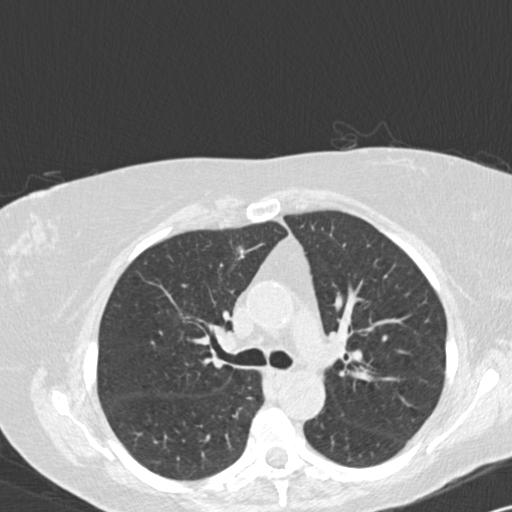
Low-dose screening chest CT, axial slice. Third annual screen. Lung window (W 1500 / L -600 HU). Standard (soft-tissue) reconstruction kernel (B30f). Slice 47 of 141 in the series. Female, age 72 years at enrolment.
- Lesion marked by an expert reader, bounding box (x1, y1, x2, y2) in pixels: (214, 232, 261, 281).
- Reader record for this screening exam (exam-level; its link to the box is not recorded): non-calcified nodule or mass ≥4 mm, right upper lobe, 8 × 8 mm, spiculated (stellate) margins, soft tissue attenuation, pre-existing on the prior screen: yes; interval growth: yes.
- Official screen result: positive, other.
- Later outcome: lung cancer diagnosed 154 days after this screen — adenocarcinoma, NOS, right upper lobe, moderately differentiated (G2), stage IA (AJCC 6th edition), 15 mm at pathology.